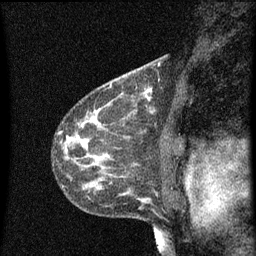
Breast MRI (dynamic contrast-enhanced), one sagittal slice; slice 35 of 60 in the series (ordered by position); dynamic contrast-enhanced series, image 2 of 3 at this slice position (ordered by acquisition); 1.5 T; TE 4.2 ms, TR 8 ms; 256 × 256 image matrix, field of view 180 × 180 mm. Female patient, age 41 years.
Annotated regions visible in this slice (semi-automatically segmented with operator editing):
- analysis volume of interest (the breast-tissue region the enhancement analysis was run in; not a lesion): box from (x=130, y=76) to (x=153, y=101) px
- tumour enhancement mask (voxels above the 70 % enhancement threshold inside the analysis volume of interest): (x=144, y=88)–(x=153, y=101)